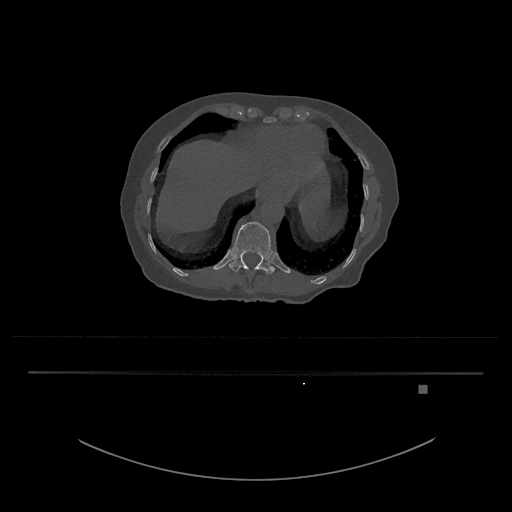
CT including the spine, one axial slice. Slice 624 of 797 in the series (ordered by position). Reconstruction kernel Br40s/3. Bone window (W 1800 / L 400 HU). 512 × 512 image matrix. Female patient, age 57 years. From the clinical record (not read from this slice): primary cancer: cervical.
Structures marked on this image (semi-automatic segmentation, software-assisted and operator-edited):
- T12 vertebra: box from (x=228, y=222) to (x=275, y=274) px